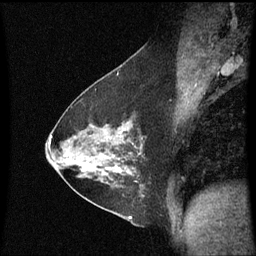
Breast MRI (dynamic contrast-enhanced), one sagittal slice; position 36 of 60 along the scan axis; dynamic contrast-enhanced series, image 2 of 3 at this slice position (ordered by acquisition); 1.5 T; TE 4.2 ms, TR 8.9 ms; 256 × 256 image matrix, field of view 200 × 200 mm. Patient: female, 54 years. From the clinical record (not read from this slice): setting: breast cancer imaged before/during neoadjuvant chemotherapy; receptor status: HER2-positive.
Structures marked on this image (semi-automatic segmentation, software-assisted and operator-edited):
- analysis volume of interest (the breast-tissue region the enhancement analysis was run in; not a lesion): bounding box [x1, y1, x2, y2] px = [102, 122, 145, 169]
- tumour enhancement mask (voxels above the 70 % enhancement threshold inside the analysis volume of interest): [121, 136, 141, 149]